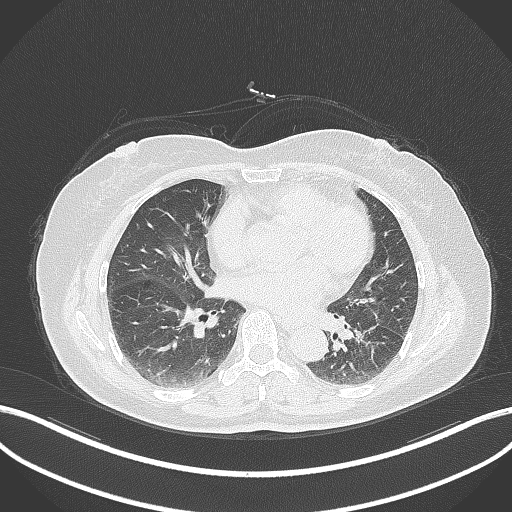
Chest CT, one axial slice; reconstruction kernel B70f; 120 kVp; lung window (W 1500 / L -600 HU); 1 mm slice thickness; 512 × 512 image matrix. Female patient, age 59 years. From the clinical record (not read from this slice): clinical TNM (as recorded): T2a N0 M0; histopathological grade: G2-3.
Structures marked on this image (rectangle marked by the reading radiologist):
- lung tumour (recorded histology: adenocarcinoma): bounding box (x1, y1, x2, y2) in pixels: (349, 319, 384, 368)